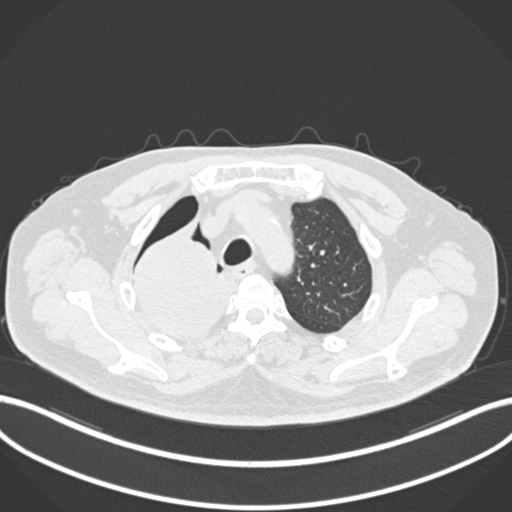
Chest CT, one axial slice; slice 169 of 218 in the series (ordered by position); reconstruction kernel B30f; 120 kVp; lung window (W 1500 / L -600 HU); 1 mm slice thickness; 512 × 512 image matrix, field of view 400 × 400 mm. Male patient, age 68 years. From the clinical record (not read from this slice): clinical TNM (as recorded): T2a N0 M0.
Outlined on this slice (bounding box drawn by a radiologist):
- lung tumour (recorded histology: adenocarcinoma): bounding box <131,222,239,343> (left, top, right, bottom; pixels)